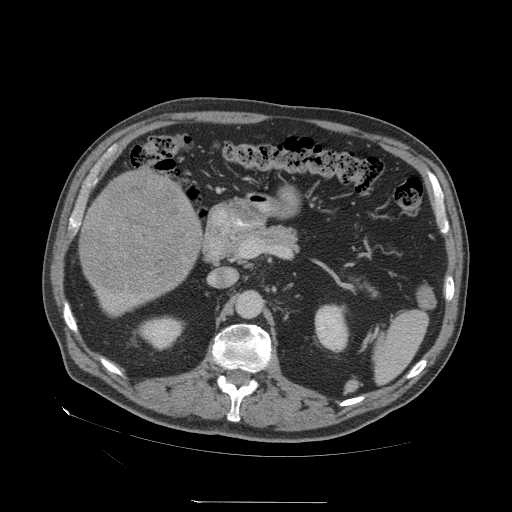
Contrast-enhanced abdominal CT (liver protocol), one axial slice; position 17 of 83 along the scan axis; reconstruction kernel STANDARD; soft-tissue window (W 400 / L 40 HU); 512 × 512 image matrix, field of view 460 × 460 mm. From the clinical record (not read from this slice): diagnosis: hepatocellular carcinoma (patient treated with transarterial chemoembolisation; whether this scan precedes or follows treatment is not stated here); TNM stage (as recorded): Stage-I; Child-Pugh class: A; tumour differentiation: well differentiated; tumour nodularity: uninodular.
Annotated regions visible in this slice (semi-automatic segmentation, software-assisted and operator-edited):
- liver parenchyma outside the tumour (the mass and vessels are separate outlines, so this box may not span the whole liver): box from (x=80, y=168) to (x=202, y=314) px
- mass: (x=82, y=172)–(x=198, y=293)